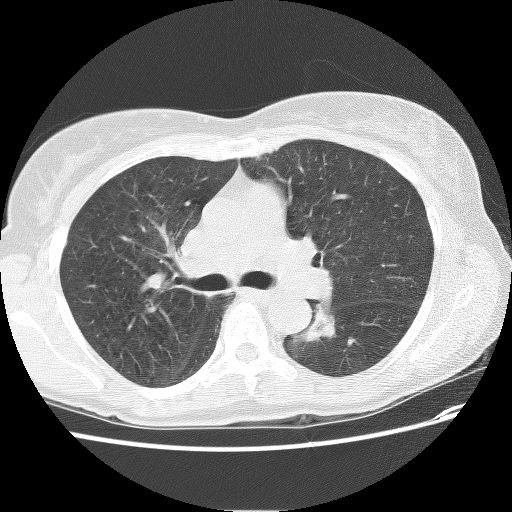
Low-dose screening chest CT, axial slice, first (baseline) screen, lung window (W 1500 / L -600 HU), 2.5 mm slice thickness, lung (sharp) reconstruction kernel (BONE), 120 kVp, slice 43 of 118 in the series. Female participant, aged 62 years at enrolment.
Expert reader's lesion annotation, bounding box (x1, y1, x2, y2) in pixels: (289, 302, 343, 344). Screening reader's record for this exam: no non-calcified nodule ≥4 mm recorded. Later outcome: lung cancer diagnosed 898 days after this screen — squamous cell carcinoma, NOS, left lower lobe, stage IIIB (AJCC 6th edition), 31 mm at pathology.